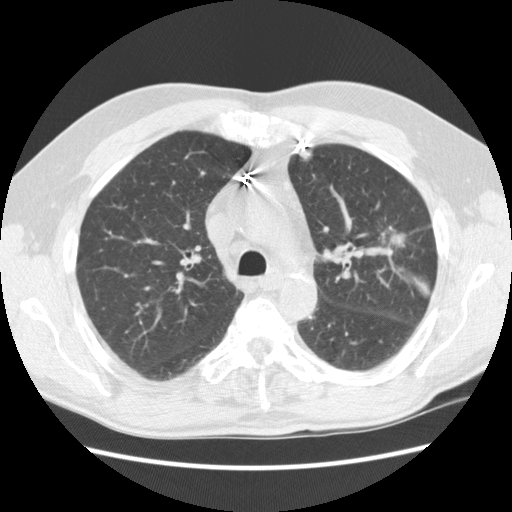
Axial slice from a low-dose chest CT screening exam, first (baseline) screen, lung window (W 1500 / L -600 HU), 120 kVp, 512 × 512 image matrix. Male, age 72 years at enrolment. Former smoker at enrolment.
Lesion marked by an expert reader, bounding box <362,214,428,260> (left, top, right, bottom; pixels). Reader record for this screening exam (exam-level; its link to the box is not recorded): non-calcified nodule or mass ≥4 mm, left upper lobe, 25 × 18 mm, spiculated (stellate) margins, soft tissue attenuation. Participant outcome: lung cancer diagnosed 35 days after this screen — adenocarcinoma, NOS, left upper lobe, well differentiated (G1), stage IIIB (AJCC 6th edition), 25 mm at pathology.